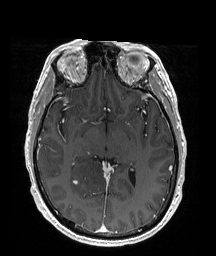
Brain MRI from a brain-tumour surgery series, one axial slice; position 103 of 176 along the scan axis; T1-weighted post-contrast; 1 mm slice thickness; 216 × 256 image matrix, field of view 211 × 250 mm. From the clinical record (not read from this slice): histopathology: Oligodendroglioma; WHO grade: 2; IDH mutation: yes.
Outlined on this slice (expert manual segmentation):
- tumour: bounding box [x1, y1, x2, y2] px = [70, 150, 111, 205]